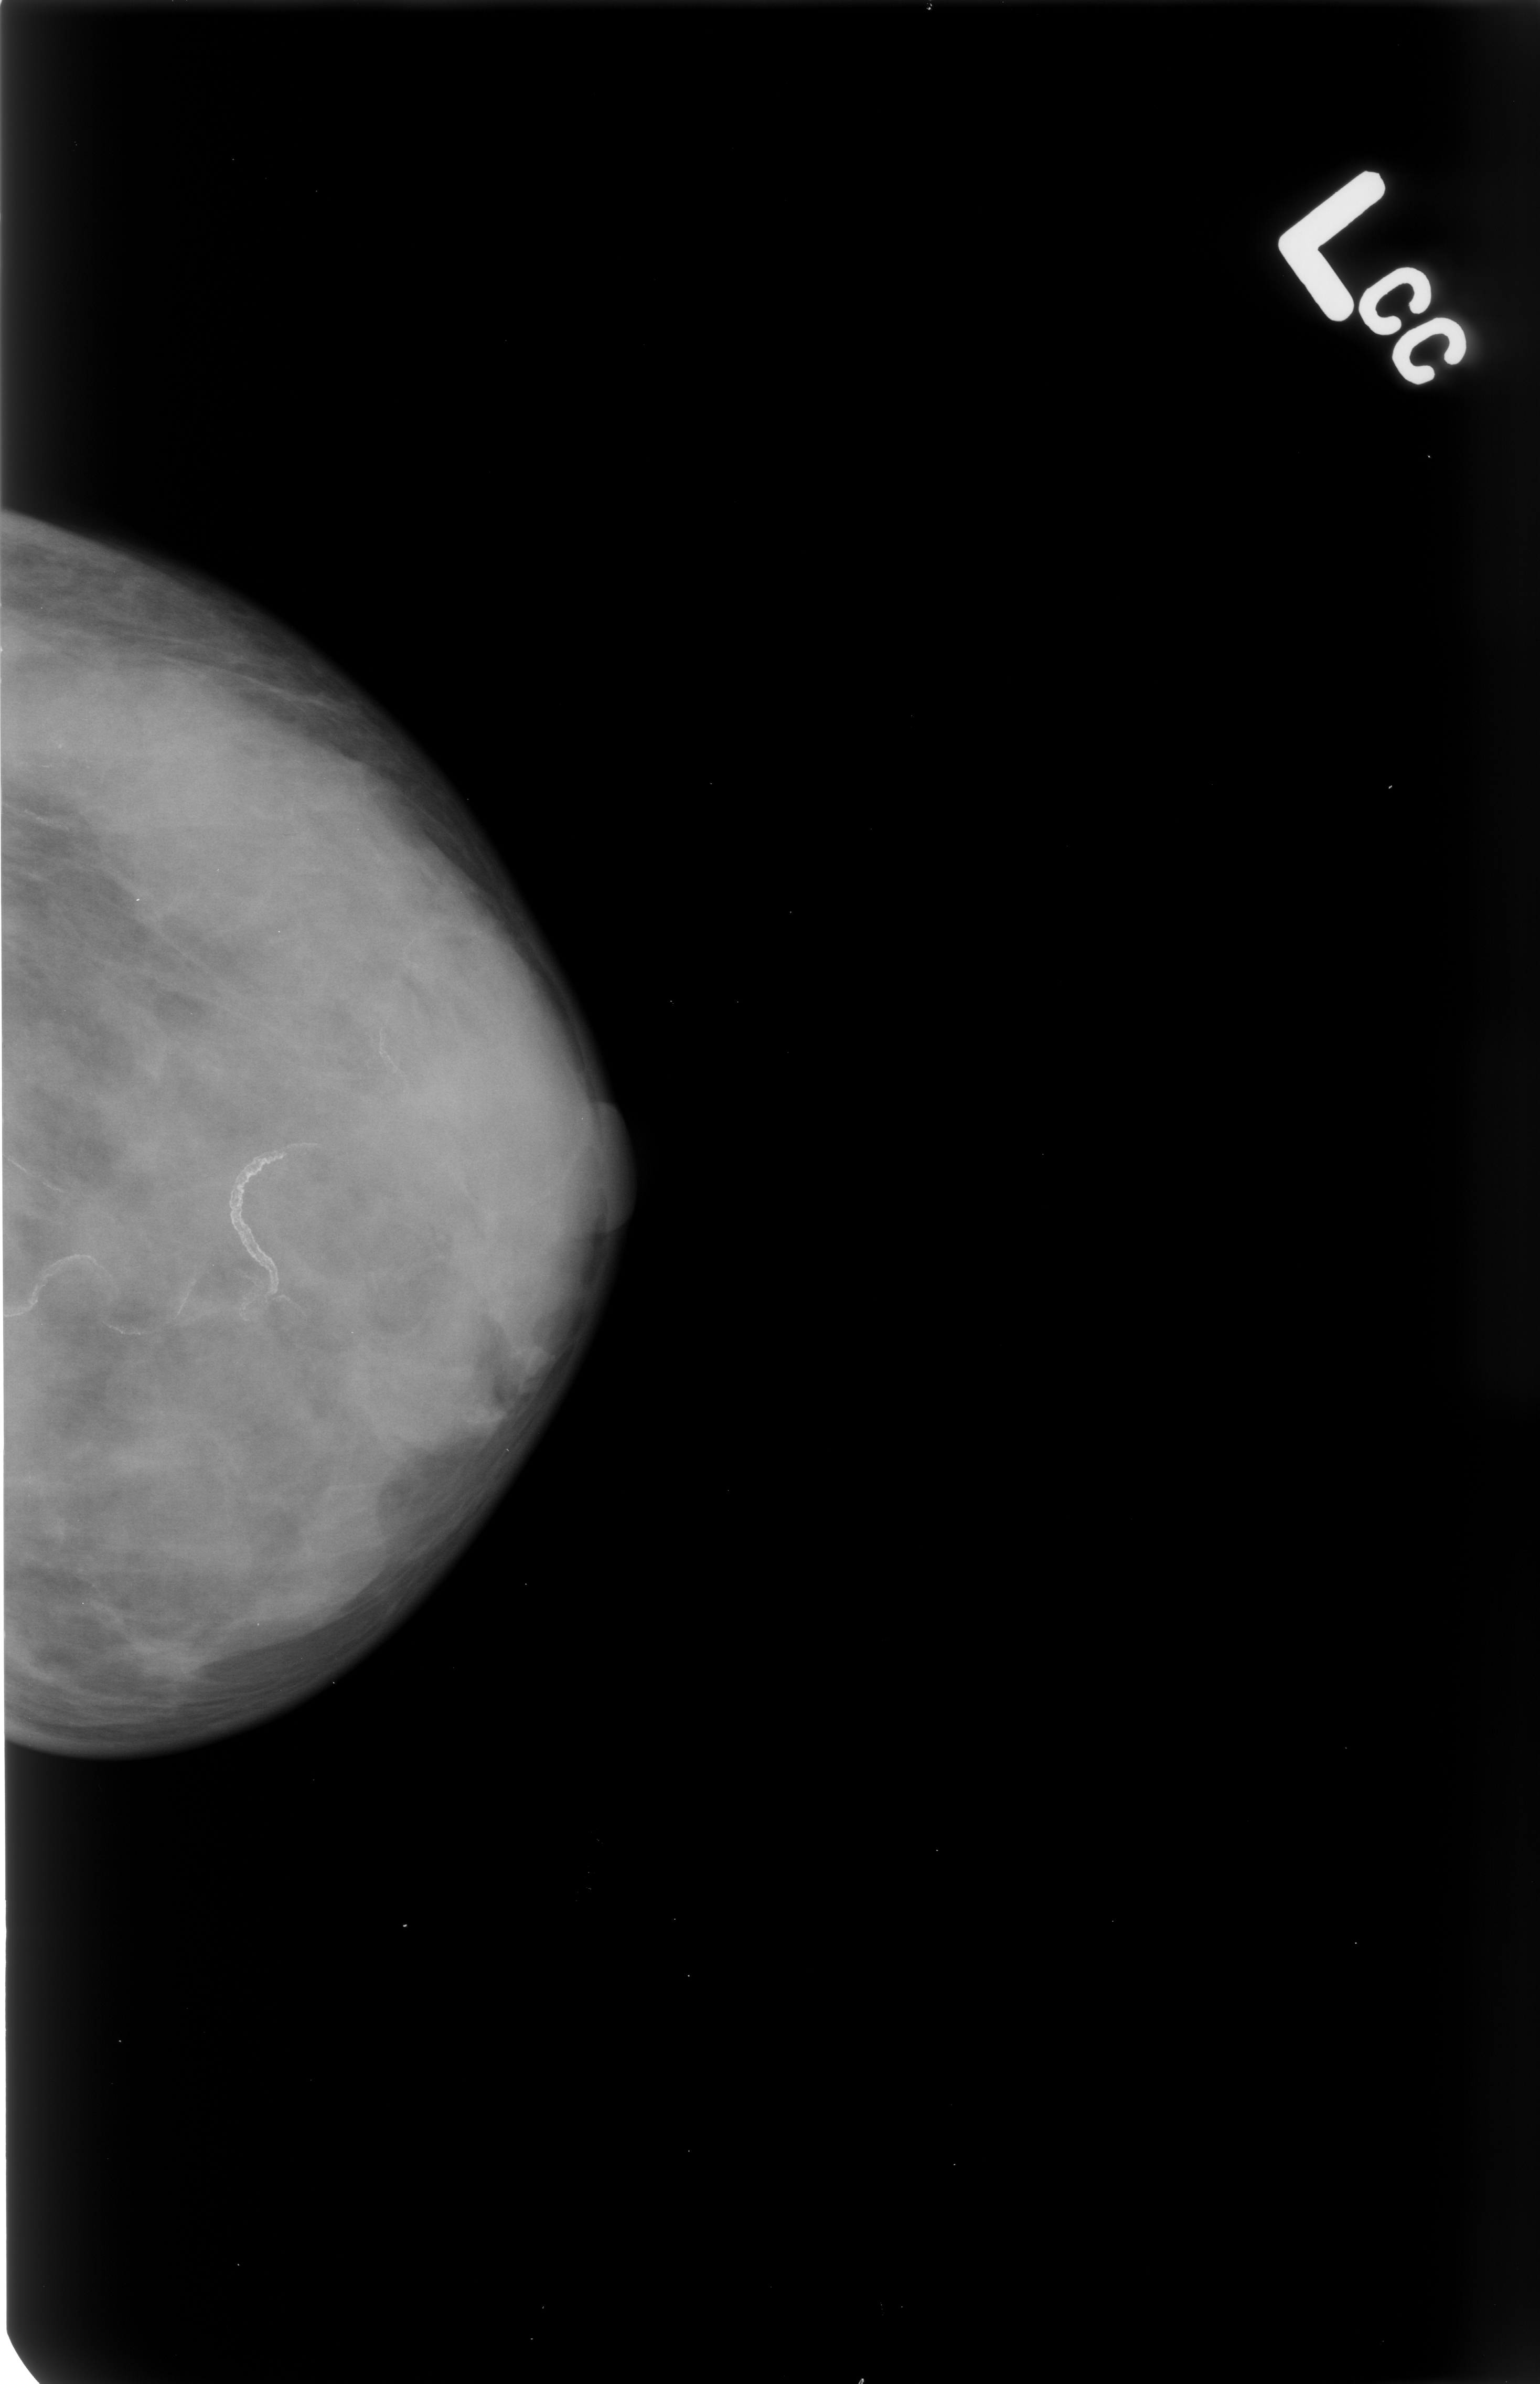
Scanned film-screen mammogram. Left breast. Craniocaudal (CC) view. 1540 × 2384 image matrix.
Expert-marked regions of interest on this film, with their recorded descriptors:
- calcifications, morphology vascular; BI-RADS assessment category 2; benign; no additional work-up was recommended (outcome (as recorded, no biopsy): benign without callback): bounding box <0,1116,312,1374> (left, top, right, bottom; pixels)